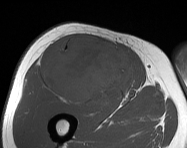
MRI of an extremity soft-tissue mass, one axial slice. Position 87 of 114 along the scan axis. MR volume resampled by the dataset authors to the PET/CT grid (not the native acquisition matrix). 187 × 148 image matrix, field of view 183 × 145 mm. Male patient. From the clinical record (not read from this slice): histological type: pleiomorphic leiomyosarcoma; grade: intermediate; site of the primary tumour: right thigh.
Outlined on this slice (expert contour drawn on MRI and transferred to this co-registered scan by the dataset authors):
- gross tumour volume including surrounding oedema: bounding box [x1, y1, x2, y2] px = [43, 36, 133, 105]
- gross tumour volume (mass): [43, 36, 133, 105]